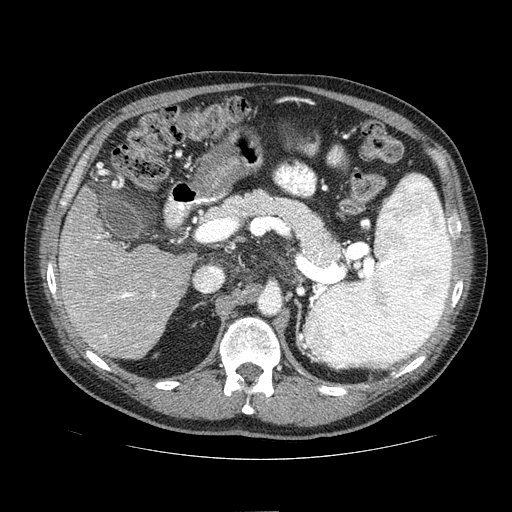
Contrast-enhanced abdominal CT (liver protocol), one axial slice; slice 35 of 81 in the series (ordered by position); 100 kVp; one of 2 acquisitions stored at this slice position; soft-tissue window (W 400 / L 40 HU); 512 × 512 image matrix, field of view 400 × 400 mm. Case-level facts recorded for this patient, not image findings: diagnosis: hepatocellular carcinoma (patient treated with transarterial chemoembolisation; whether this scan precedes or follows treatment is not stated here); TNM stage (as recorded): Stage-IIIA; Child-Pugh class: A; tumour differentiation: well differentiated; tumour nodularity: multinodular.
Structures marked on this image (semi-automatic segmentation, software-assisted and operator-edited):
- liver parenchyma outside the tumour (the mass and vessels are separate outlines, so this box may not span the whole liver): bounding box [x1, y1, x2, y2] px = [58, 186, 196, 358]
- liver vessels: [64, 235, 157, 347]